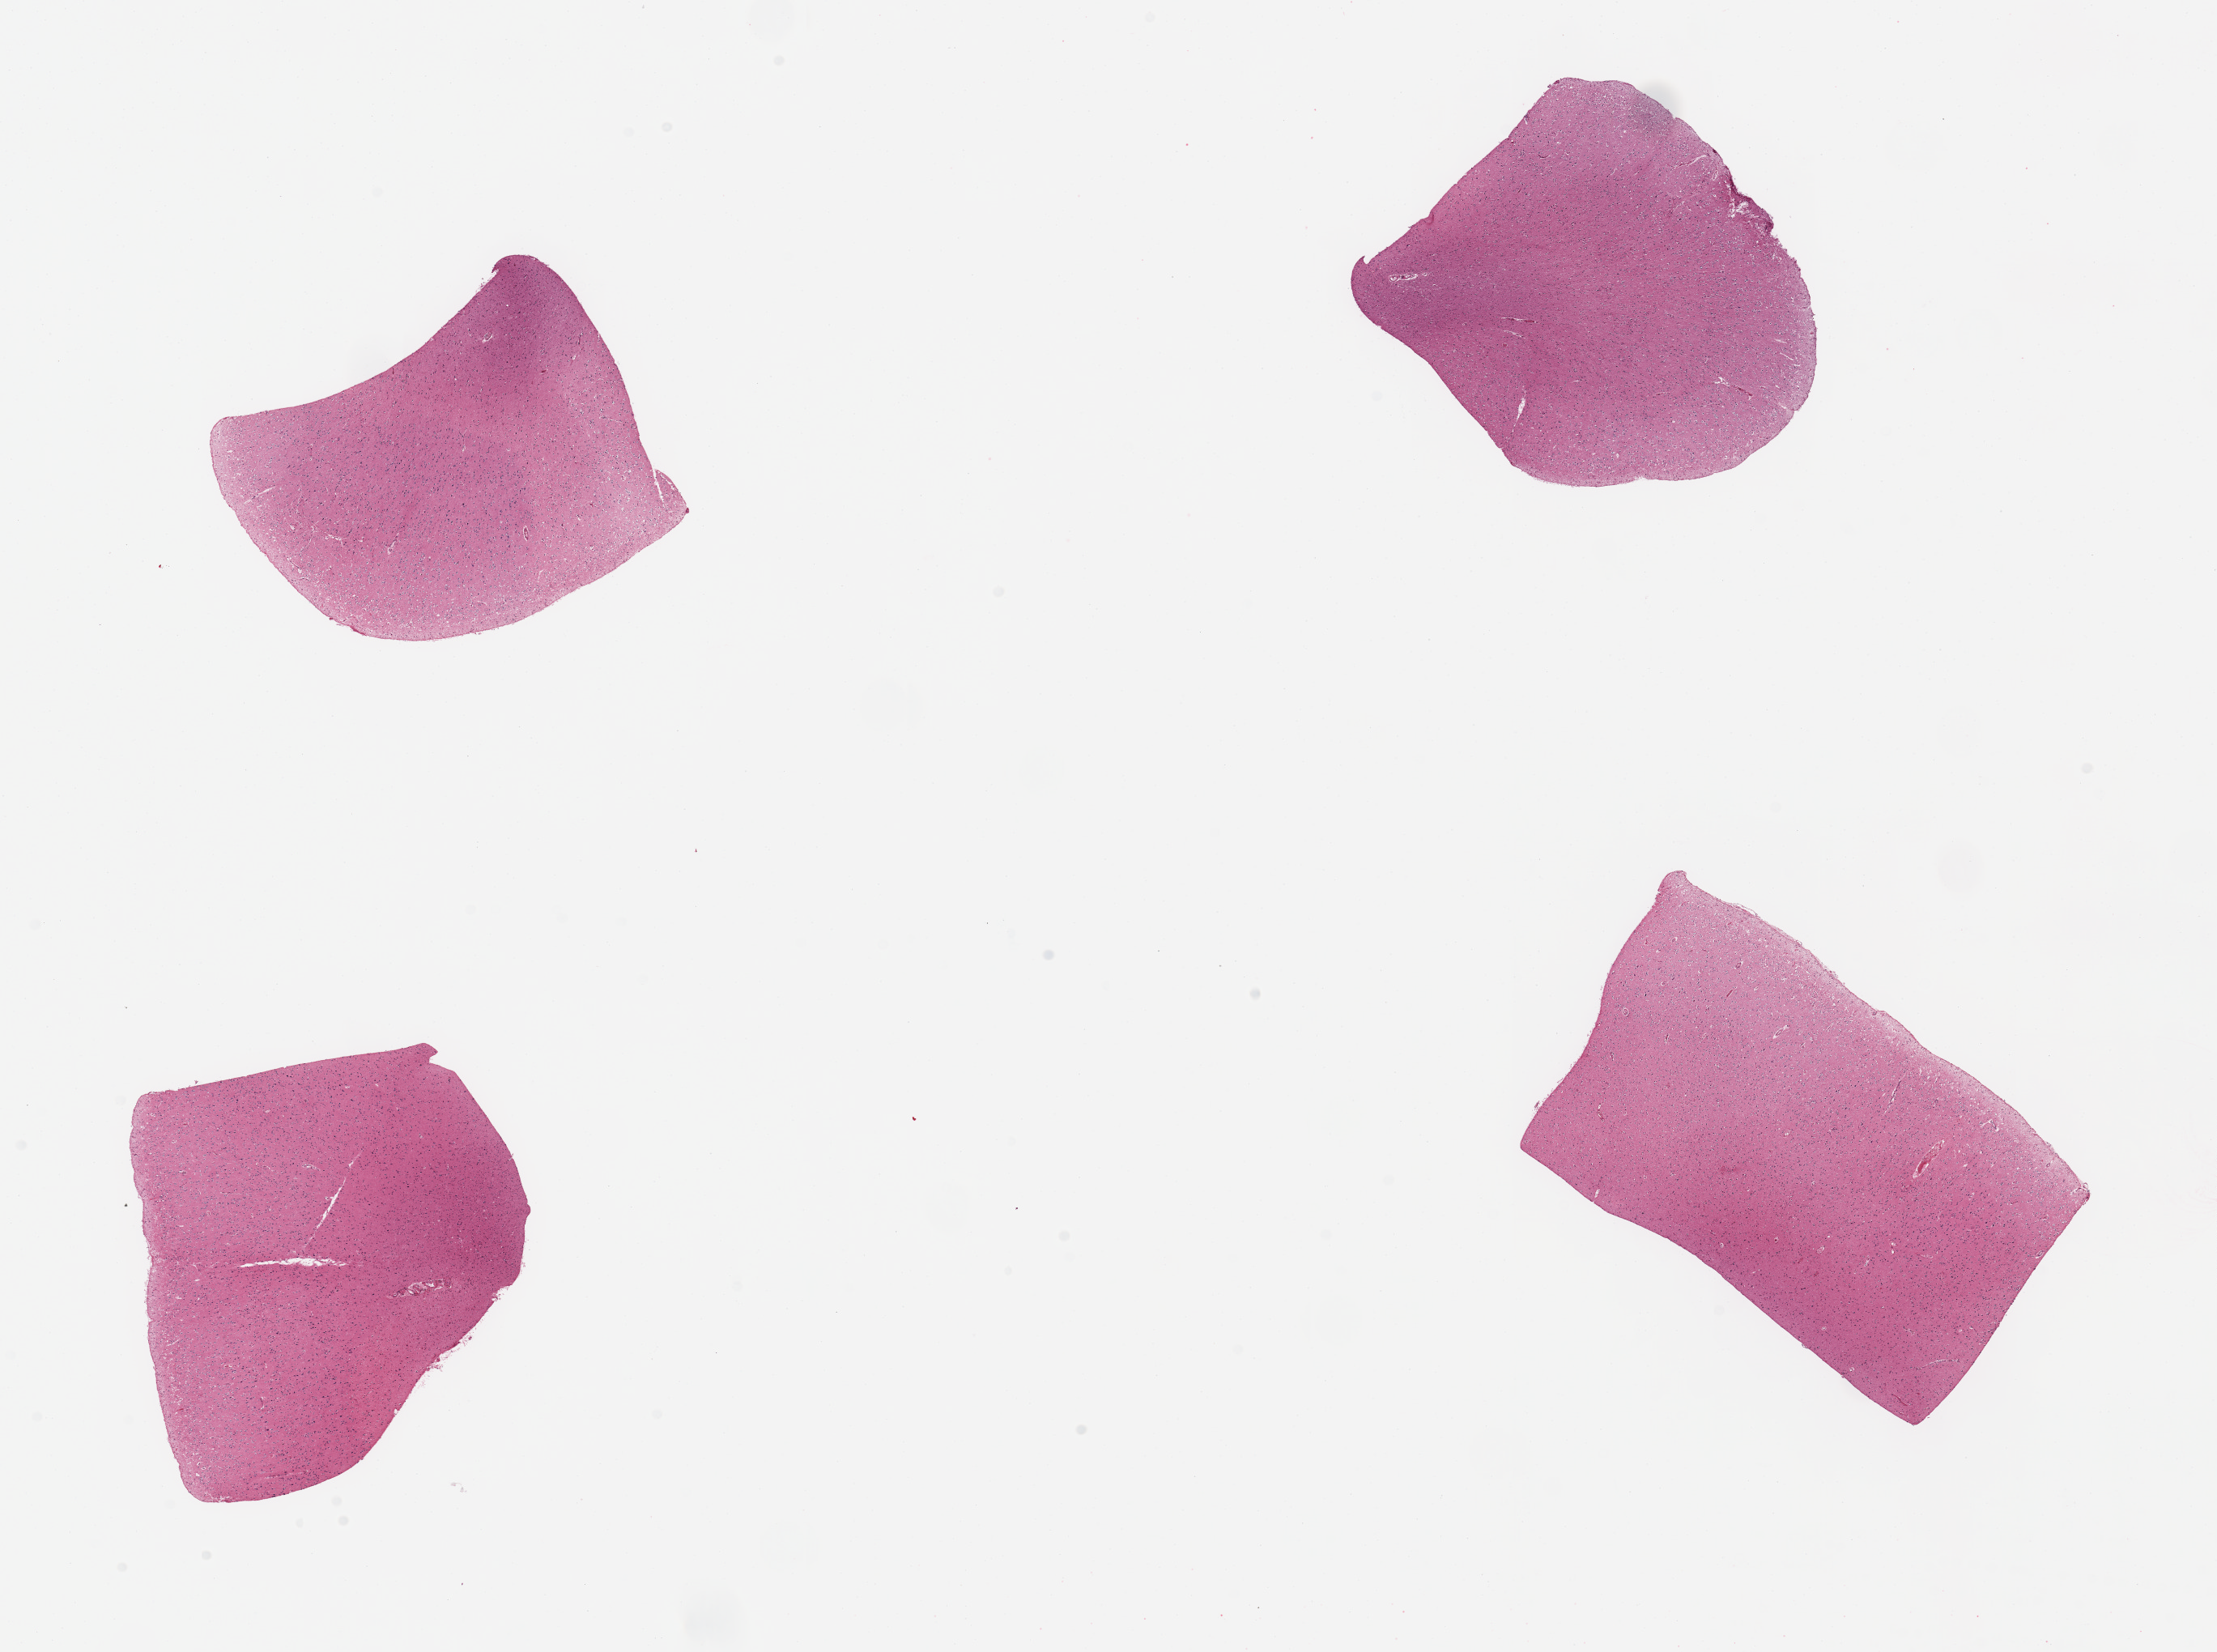
Digitized haematoxylin and eosin-stained section, brightfield, low-resolution overview of the scanned area, about 21.7 x 16.1 mm, PAXgene-fixed, paraffin-embedded tissue, target tissue: cerebral cortex, tissue donor sample. Donor: female.
Reviewer comment on this tissue sample: 4 pieces.